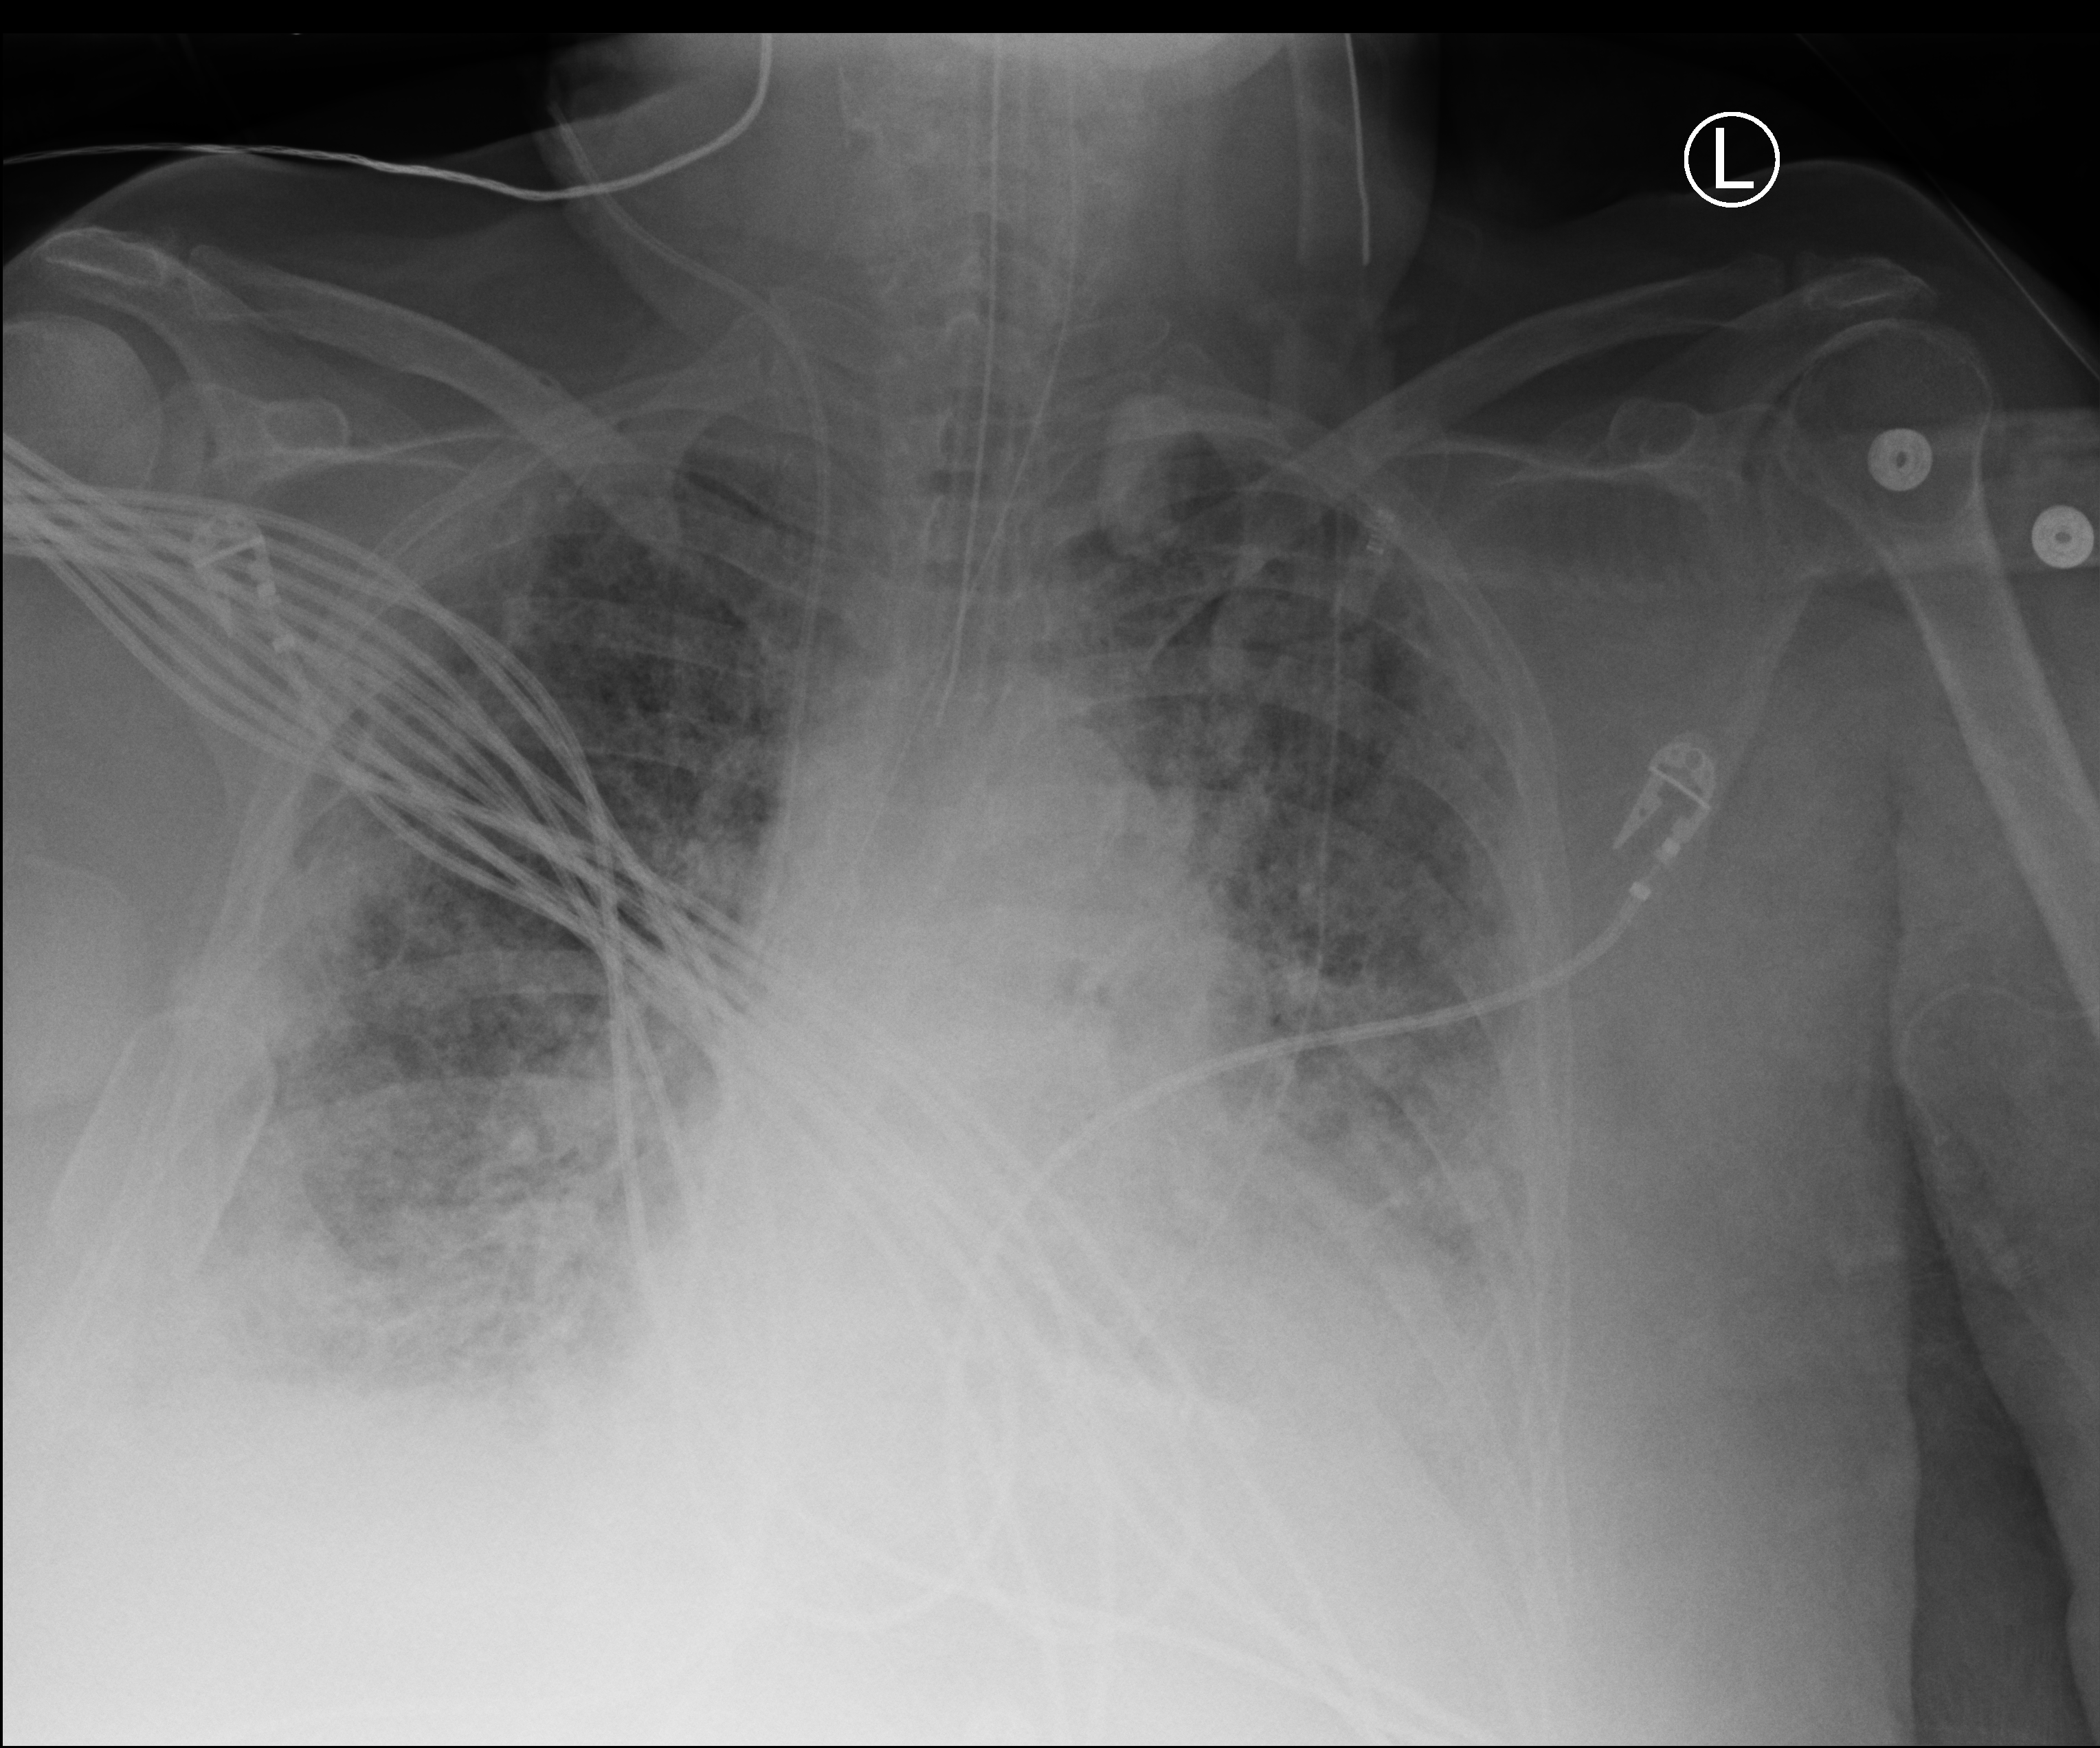
Portable chest radiograph; anteroposterior (AP) projection. Female patient hospitalised with COVID-19, age 60–74 years.
From the hospital-stay record, not from the radiograph (when in the stay this image was taken is not recorded): chronic kidney disease (admission record): no.